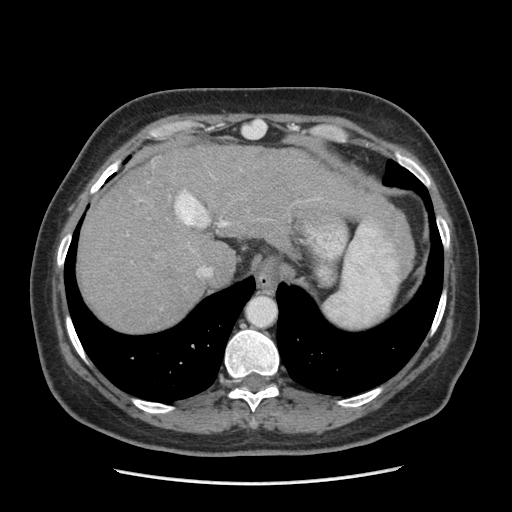
Contrast-enhanced abdominal CT (liver protocol), one axial slice. Slice 165 of 185 in the series (ordered by position). Soft-tissue window (W 400 / L 40 HU). 2.5 mm slice thickness. 512 × 512 image matrix, field of view 360 × 360 mm. Case-level facts recorded for this patient, not image findings: diagnosis: hepatocellular carcinoma (patient treated with transarterial chemoembolisation; whether this scan precedes or follows treatment is not stated here); TNM stage (as recorded): Stage-I; Child-Pugh class: A; tumour nodularity: uninodular.
Annotated regions visible in this slice (semi-automatically segmented with operator editing):
- abdominal aorta: bounding box <247,296,275,326> (left, top, right, bottom; pixels)
- liver parenchyma outside the tumour (the mass and vessels are separate outlines, so this box may not span the whole liver): <76,144,368,332>
- mass: <132,187,155,217>
- liver vessels: <200,221,228,276>